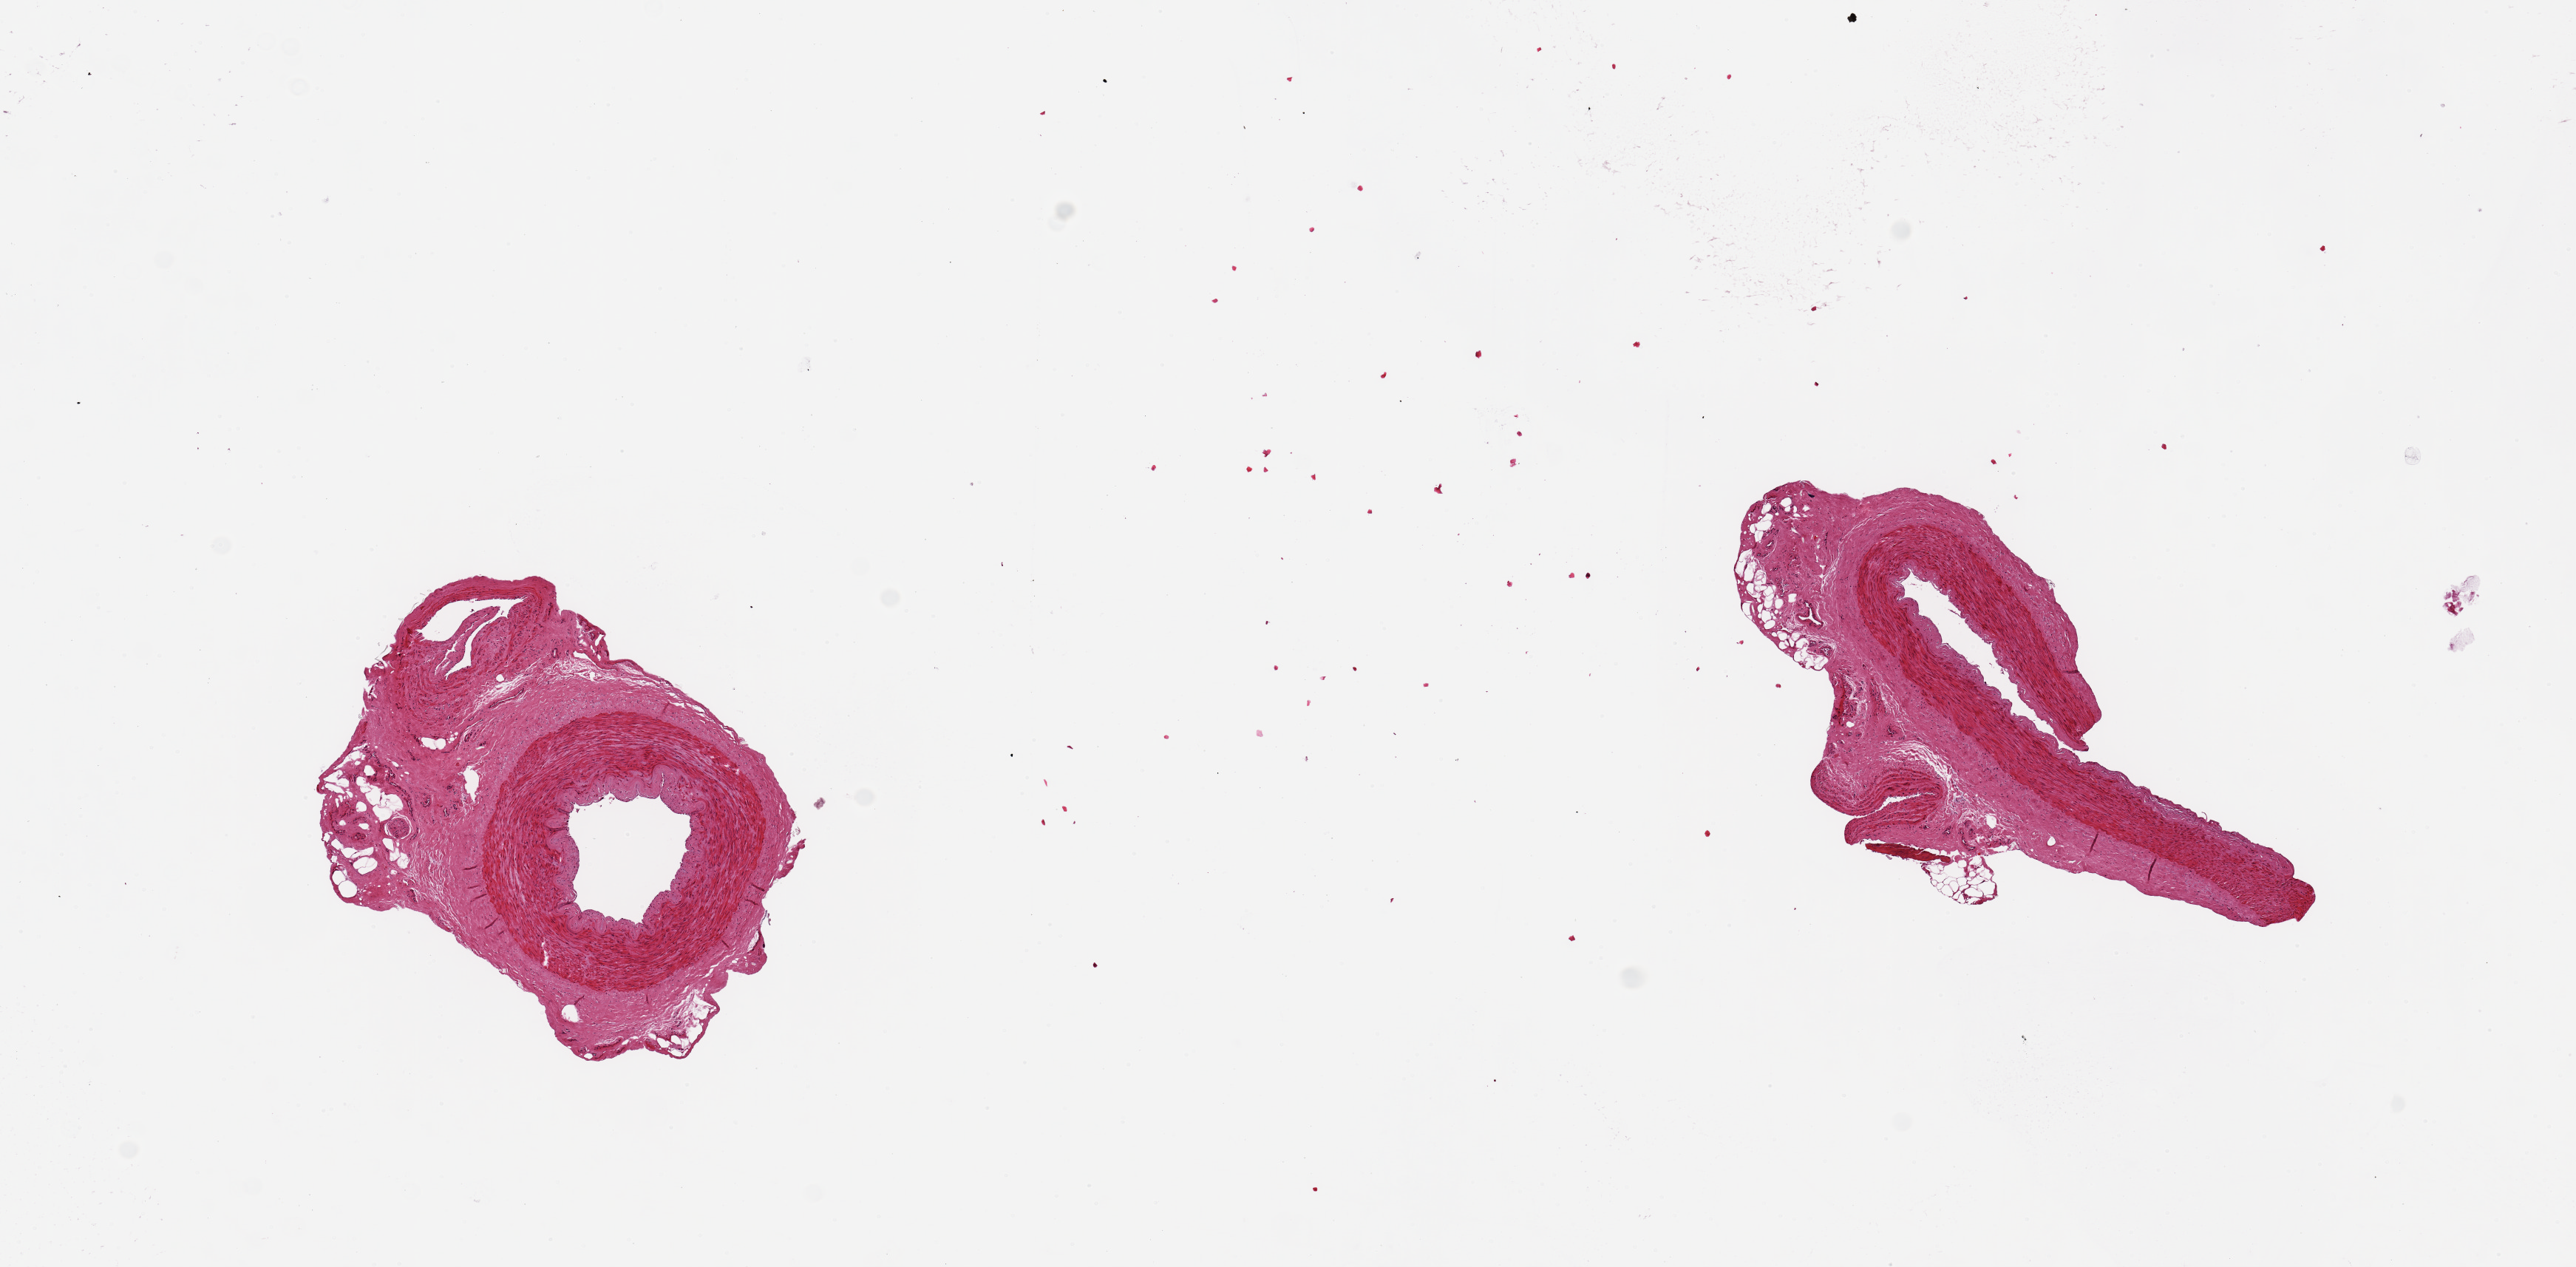
Haematoxylin and eosin whole-slide image, brightfield — shown as a low-resolution overview of the whole scanned area (about 13.8 x 6.8 mm, from a 20x scan); PAXgene-fixed paraffin-embedded (PFPE) section; target tissue: tibial artery; donor tissue sample. Donor sex: male.
Pathologist's review note for this sample: 2 pieces, 3x2 & 3.5x2mm;1, 2mm artery and 0.6 mm vein in each; <10% adipose.